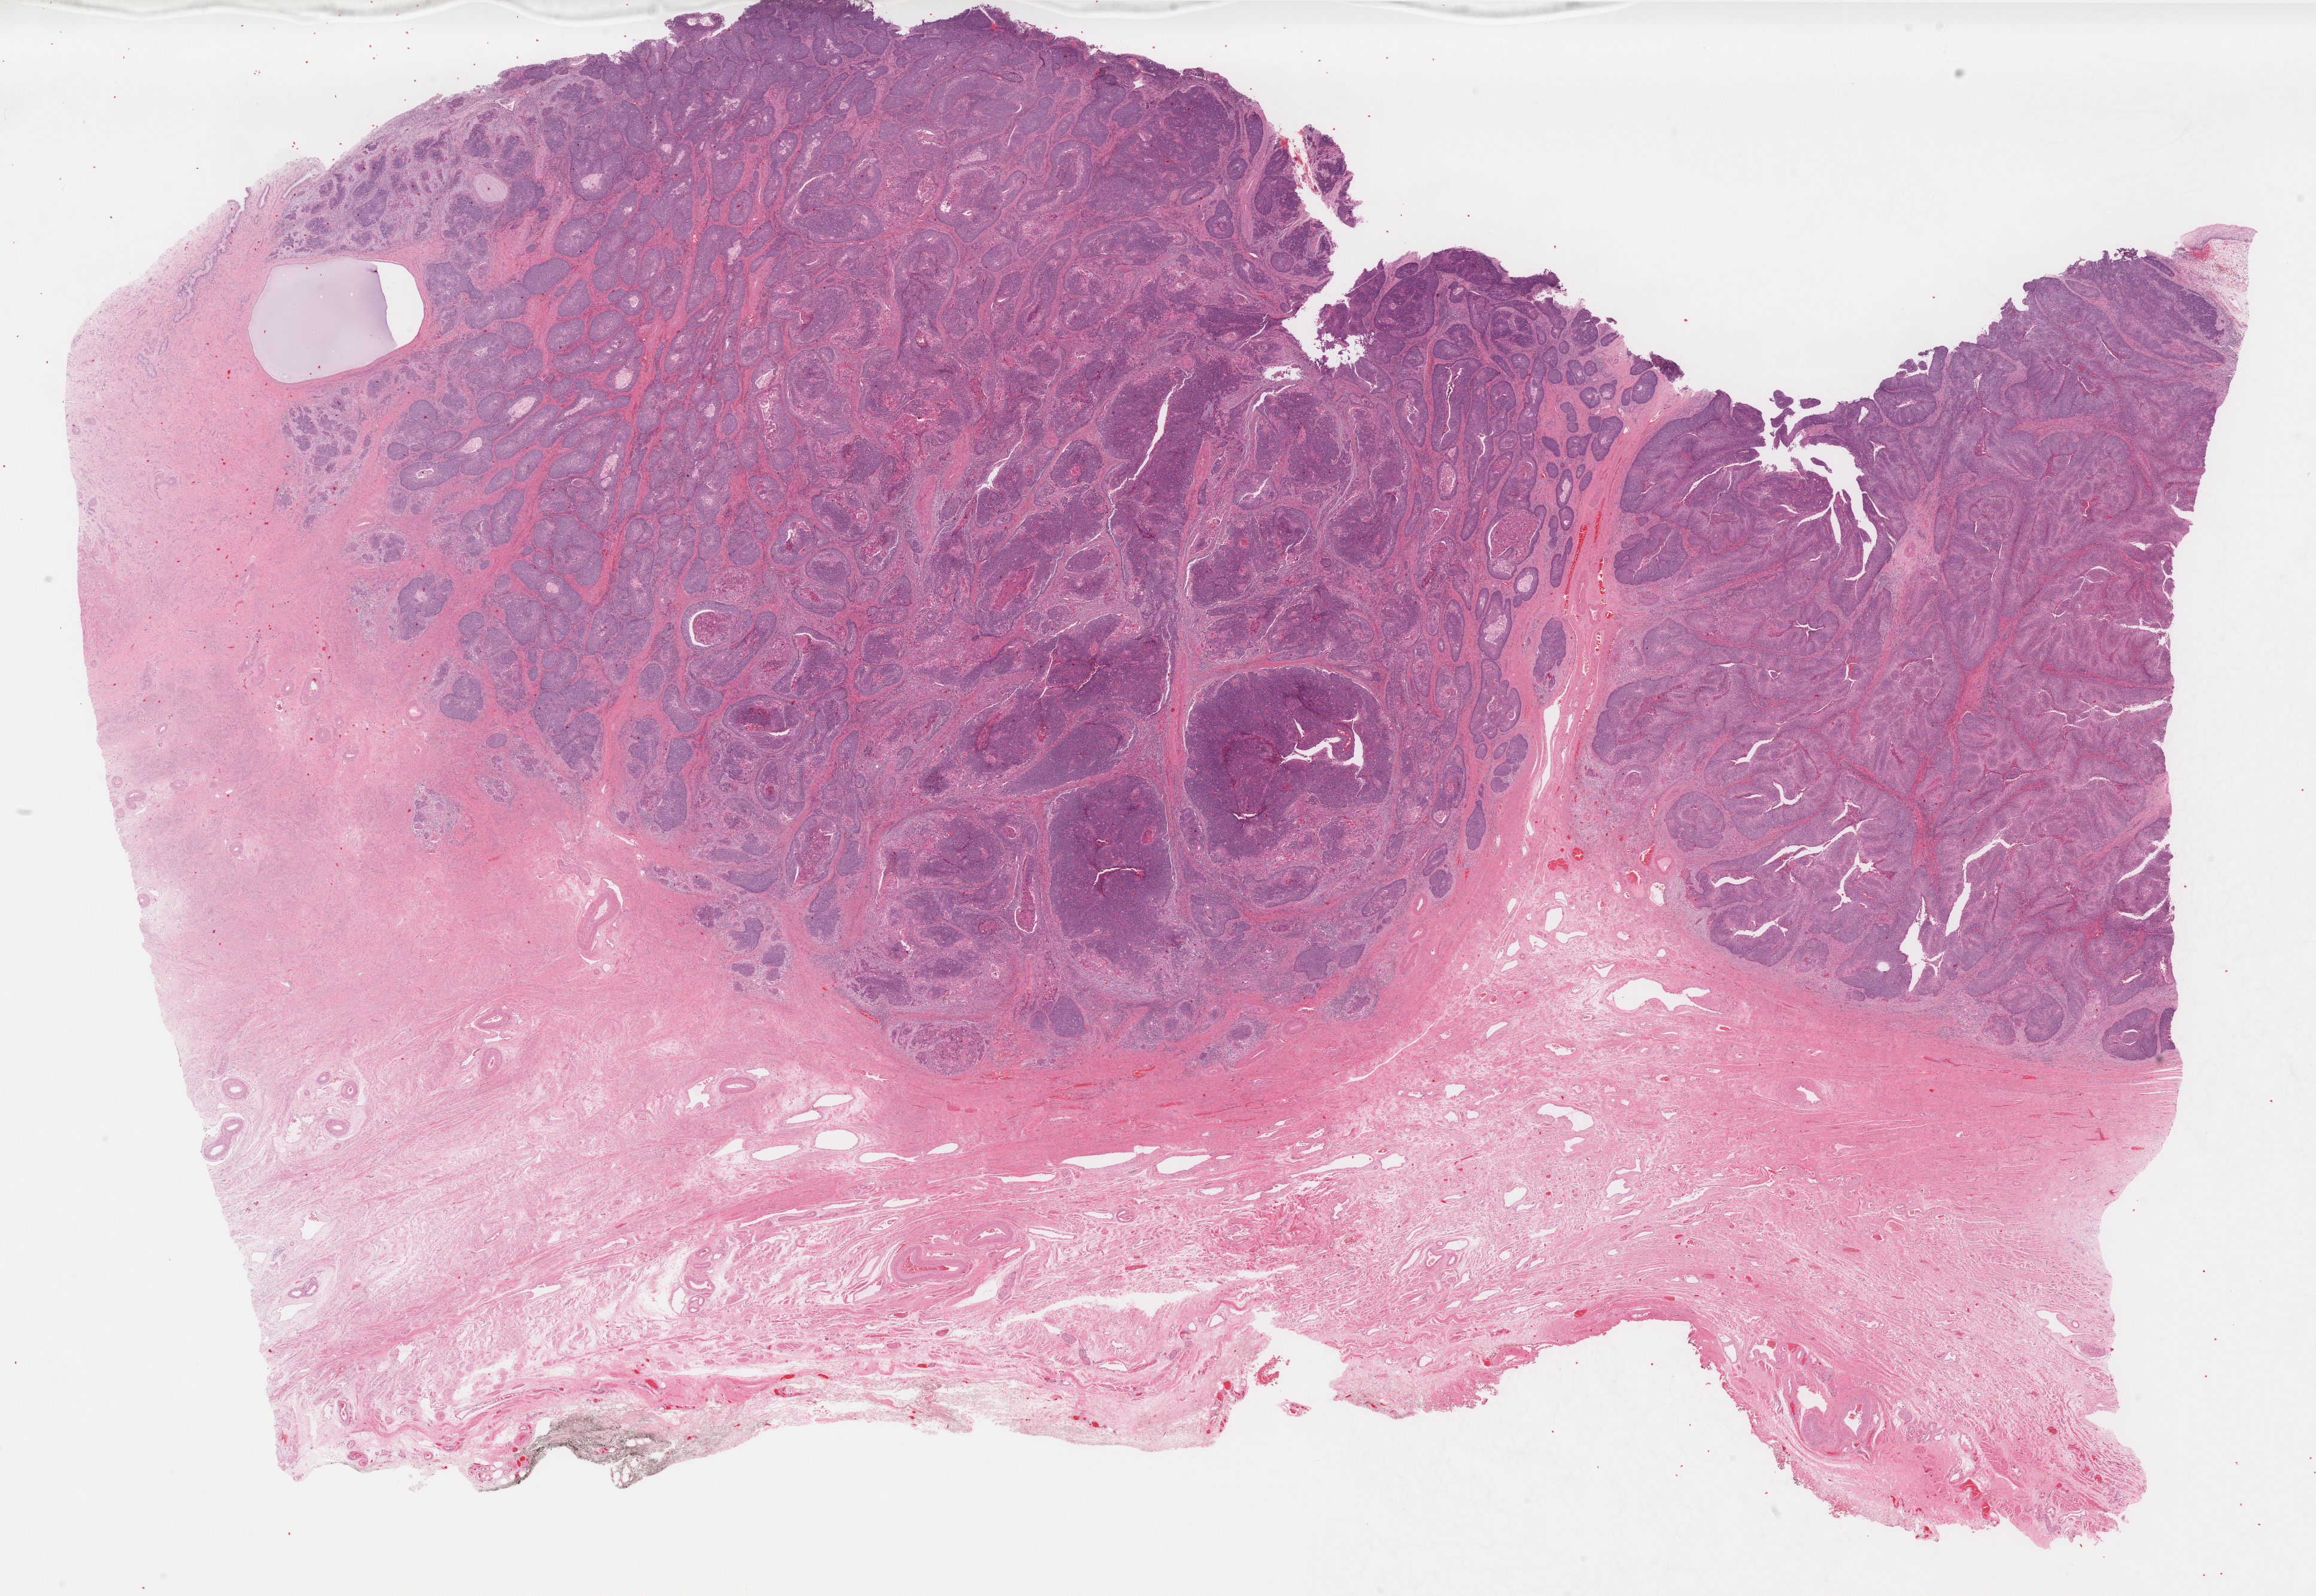
Hematoxylin and eosin (H&E) stained whole-slide image, shown as a low-resolution overview of the whole scanned area (about 31.0 x 21.3 mm, slide scanned at 40x); FFPE section; cervix, primary tumour sample. Female, age 53 years at initial diagnosis. Histologic grade: G2 (moderately differentiated).
* pathologic diagnosis: Squamous cell carcinoma, NOS (cervix uteri)
* FIGO stage: IB
* lymph nodes positive (case pathology): 0 of 59 examined